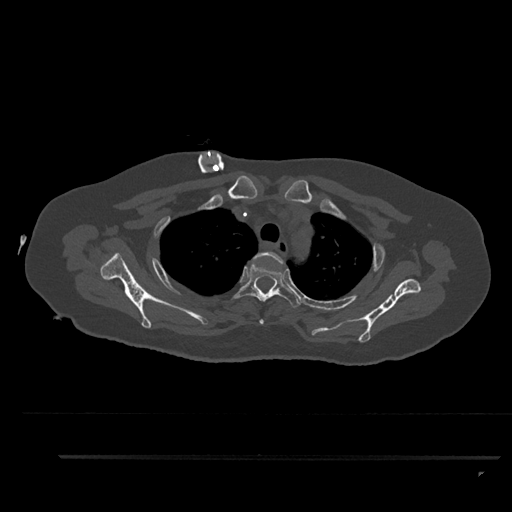
CT including the spine, one axial slice. Reconstruction kernel Br40s/3. Bone window (W 1800 / L 400 HU). 0.5 mm slice thickness. 512 × 512 image matrix, field of view 408 × 408 mm. Female patient, age 44 years. Case-level facts recorded for this patient, not image findings: primary cancer: renal.
Outlined on this slice (semi-automatic segmentation, software-assisted and operator-edited):
- T2 vertebra: bounding box <253,252,284,324> (left, top, right, bottom; pixels)
- T3 vertebra: <233,261,302,308>